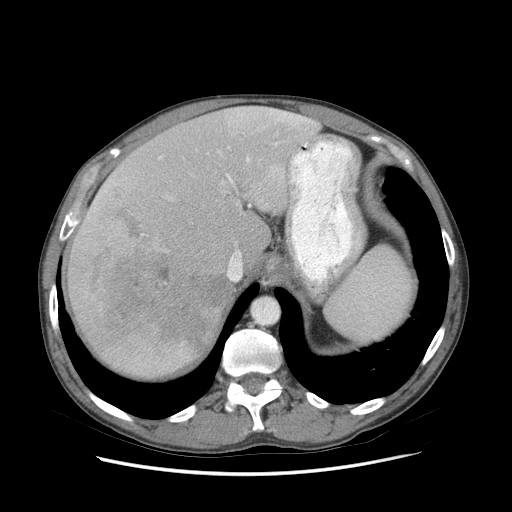
Contrast-enhanced abdominal CT (liver protocol), one axial slice. Slice 60 of 89 in the series (ordered by position). 140 kVp. Soft-tissue window (W 400 / L 40 HU). 2.5 mm slice thickness. 512 × 512 image matrix, field of view 380 × 380 mm. From the clinical record (not read from this slice): diagnosis: hepatocellular carcinoma (patient treated with transarterial chemoembolisation; whether this scan precedes or follows treatment is not stated here); TNM stage (as recorded): Stage-IIIB; Child-Pugh class: A; tumour differentiation: moderately differentiated.
Structures marked on this image (semi-automatically segmented with operator editing):
- liver parenchyma outside the tumour (the mass and vessels are separate outlines, so this box may not span the whole liver): bounding box [x1, y1, x2, y2] px = [66, 106, 318, 378]
- mass: [70, 205, 227, 355]
- liver vessels: [94, 109, 308, 281]